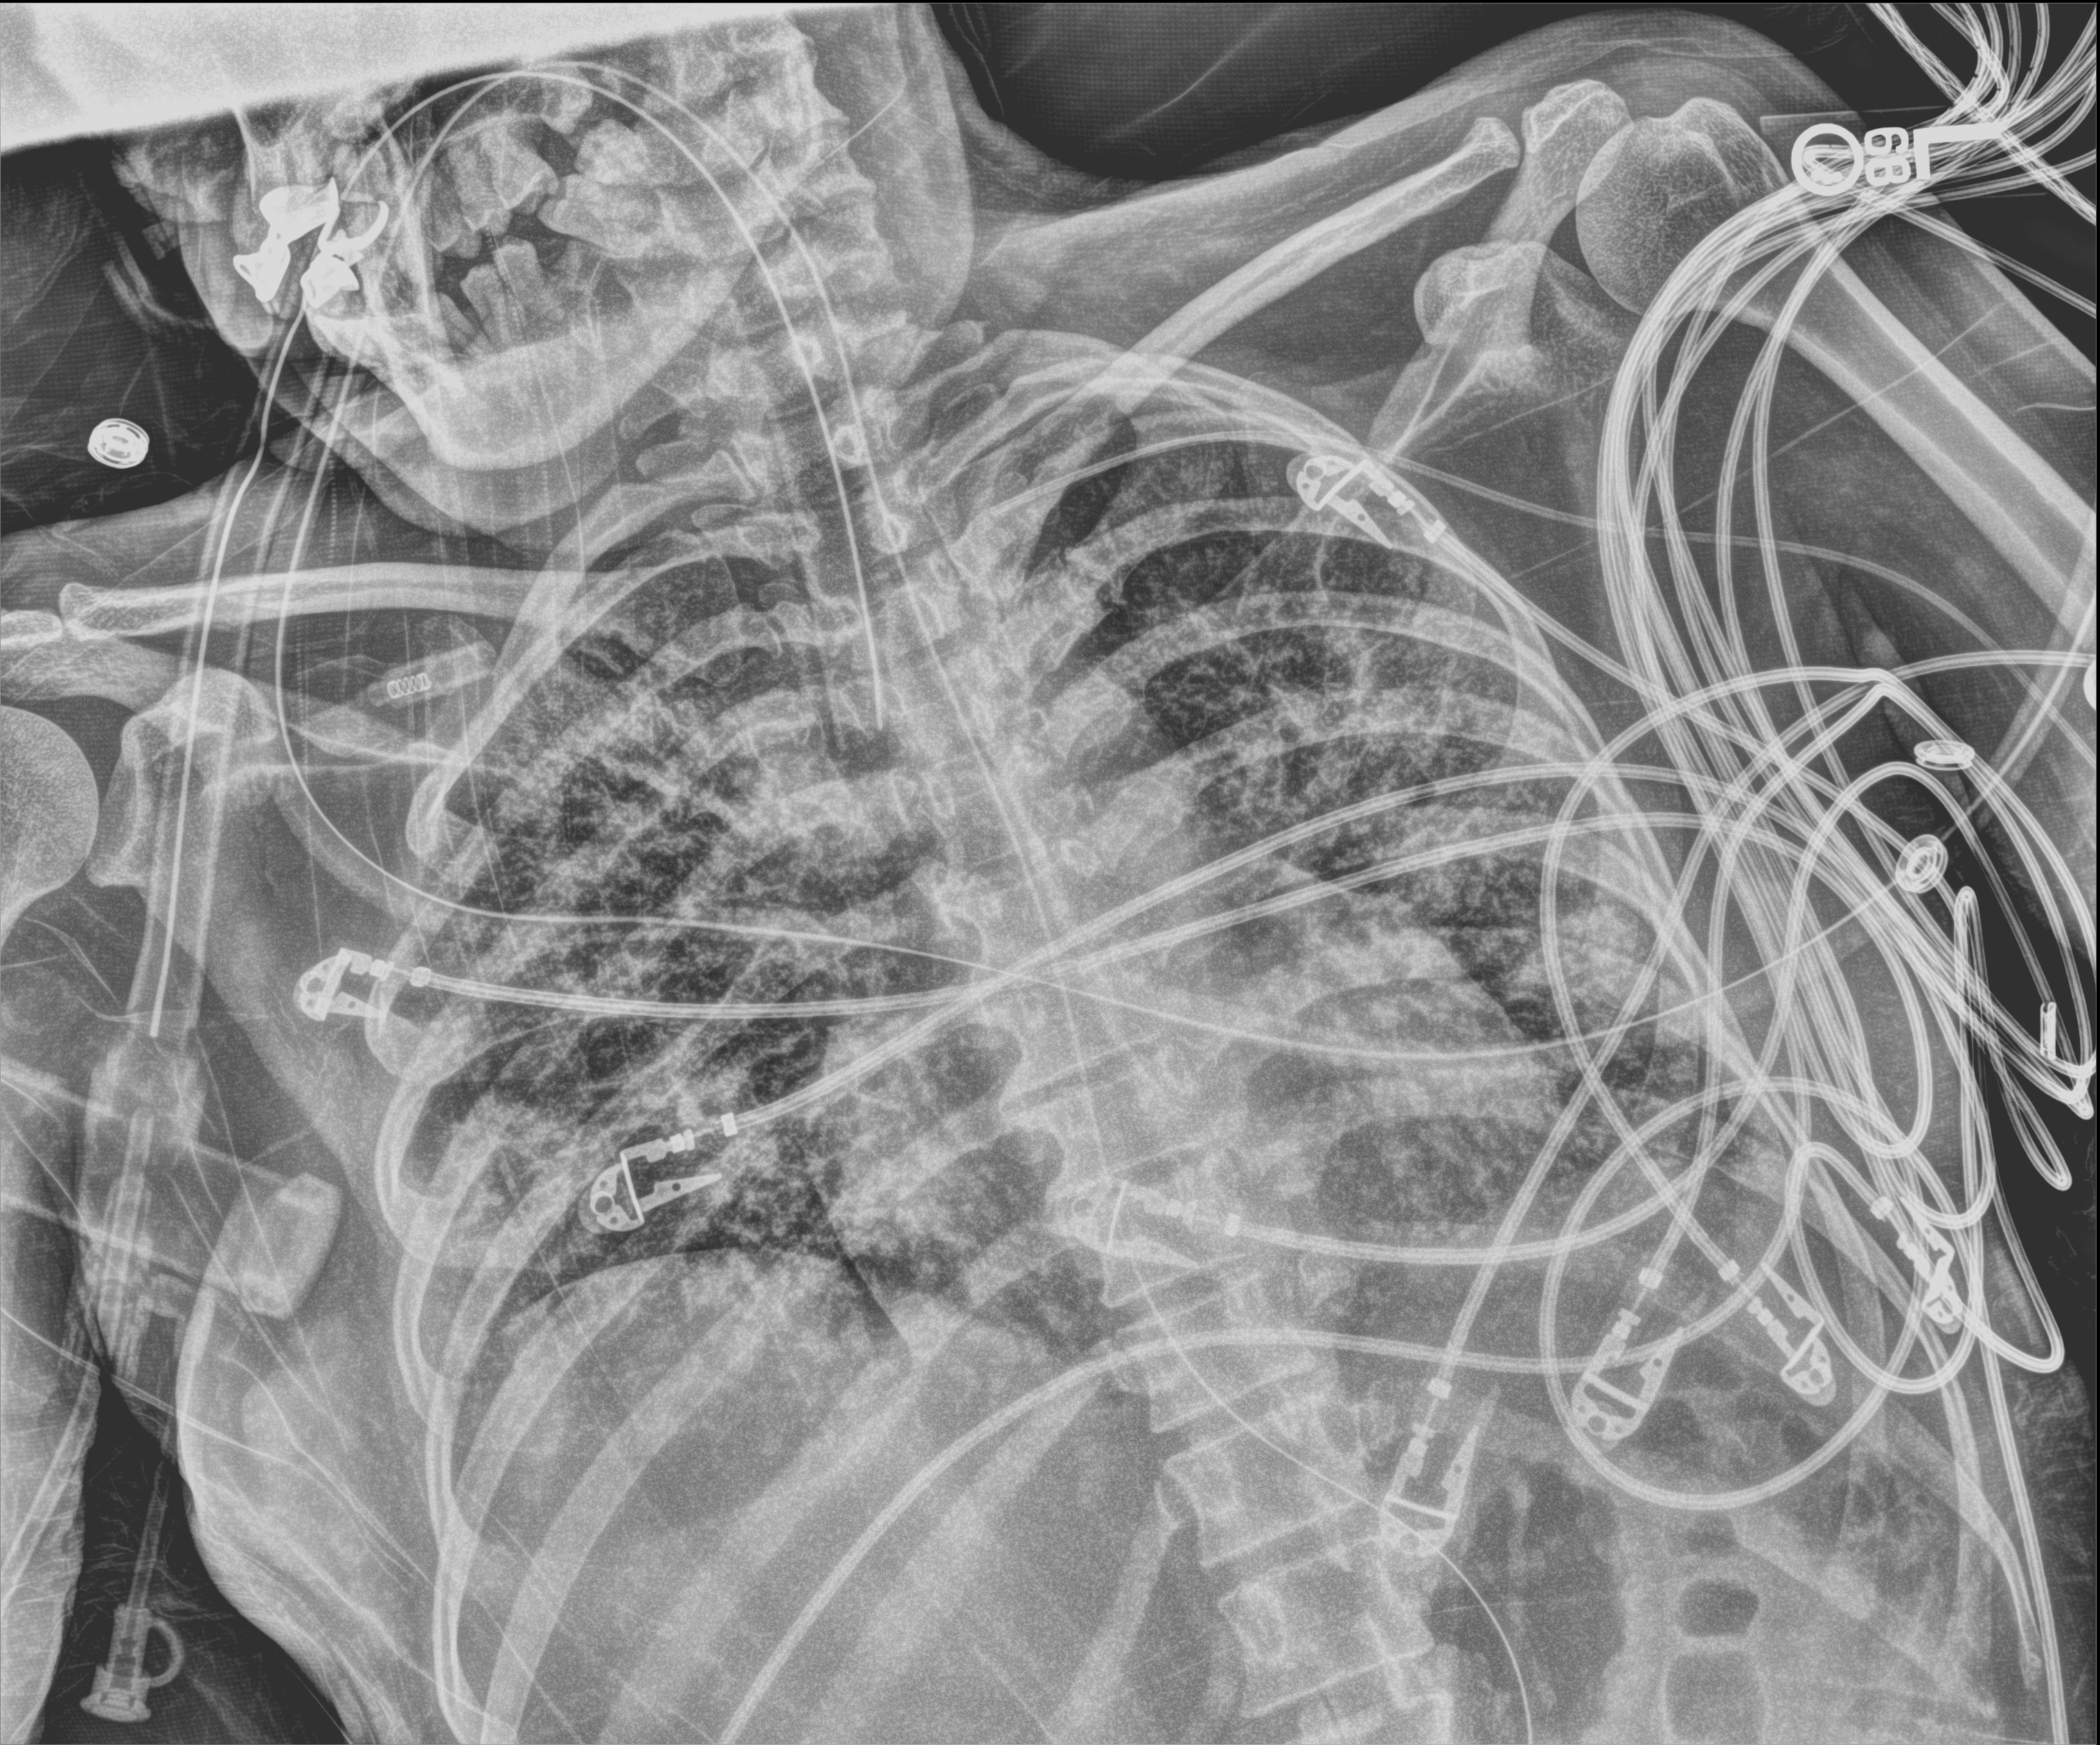
Portable chest radiograph; anteroposterior (AP) projection. Female patient hospitalised with COVID-19, age 18–59 years.
Hospital-stay facts (about this admission, not read from this image; timing relative to this image not recorded): admitted to intensive care during this hospital stay: yes.